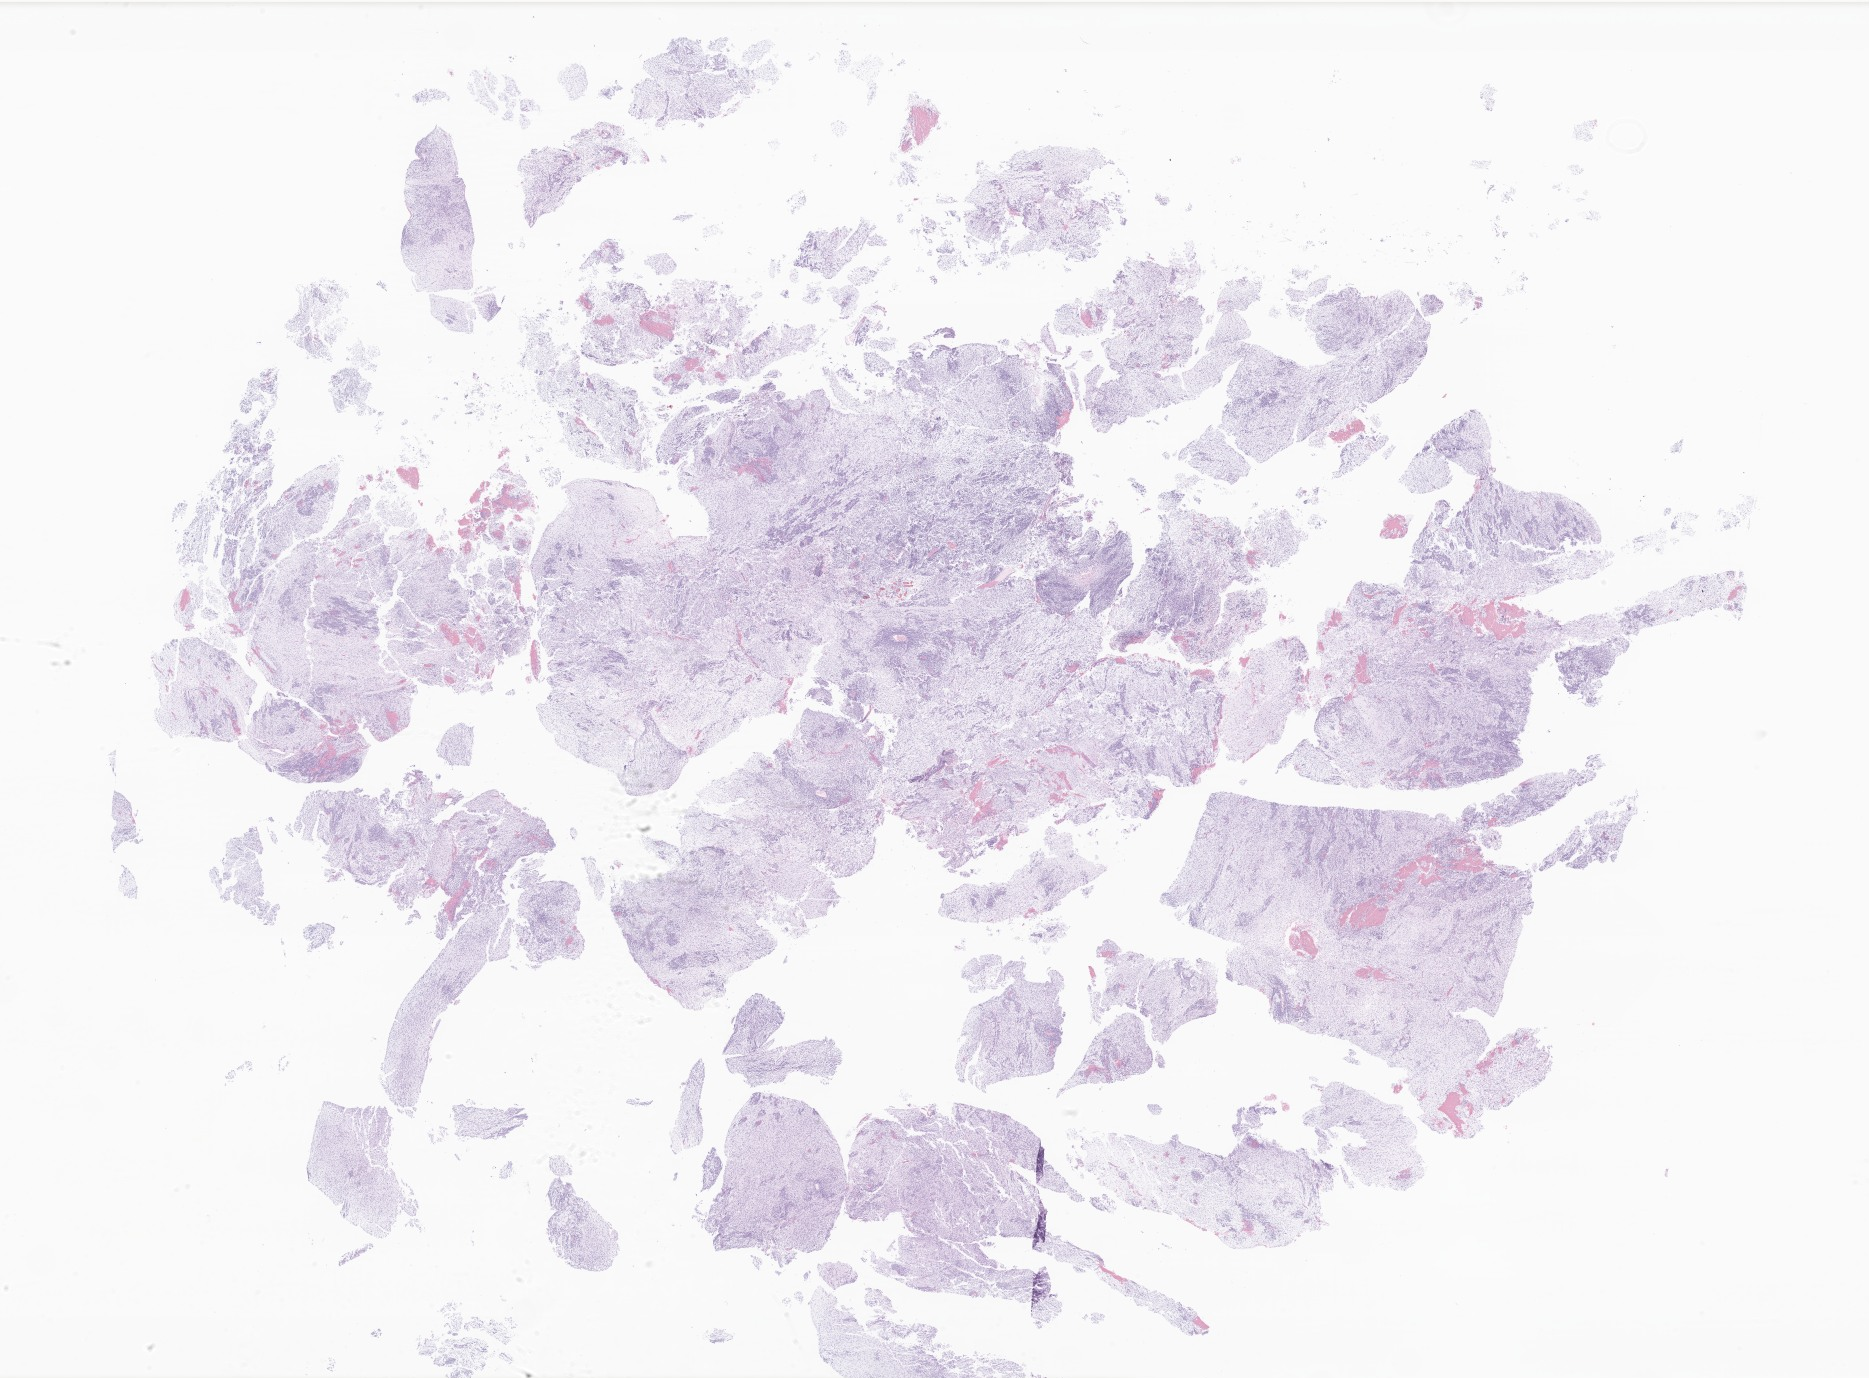
Digitized hematoxylin and eosin (H&E)-stained section of tumor tissue from the brain — low-resolution overview of the scanned area, about 31.5 x 23.2 mm. FFPE section. Patient: female, age 673 days (about 1.8 years).
Diagnosis: CNS embryonal tumor, NOS.